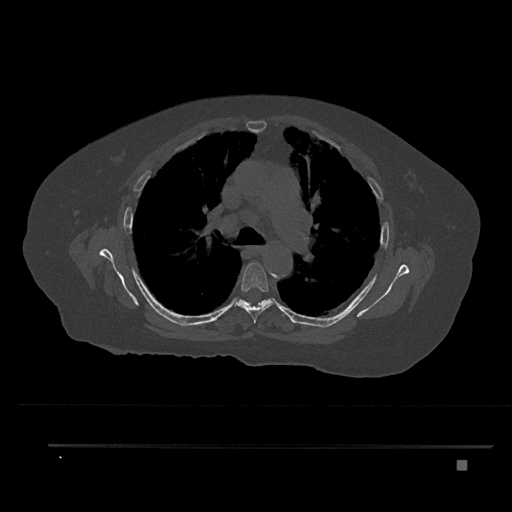
CT including the spine, one axial slice. Position 558 of 797 along the scan axis. 120 kVp. Bone window (W 1800 / L 400 HU). 512 × 512 image matrix. Patient: female, 76 years. Case-level facts recorded for this patient, not image findings: primary cancer: lung; vertebrae with lytic lesions (as recorded): T11, L3.
Structures marked on this image (semi-automatic segmentation, software-assisted and operator-edited):
- T5 vertebra: bounding box [x1, y1, x2, y2] px = [234, 262, 275, 324]
- T6 vertebra: [235, 298, 288, 316]